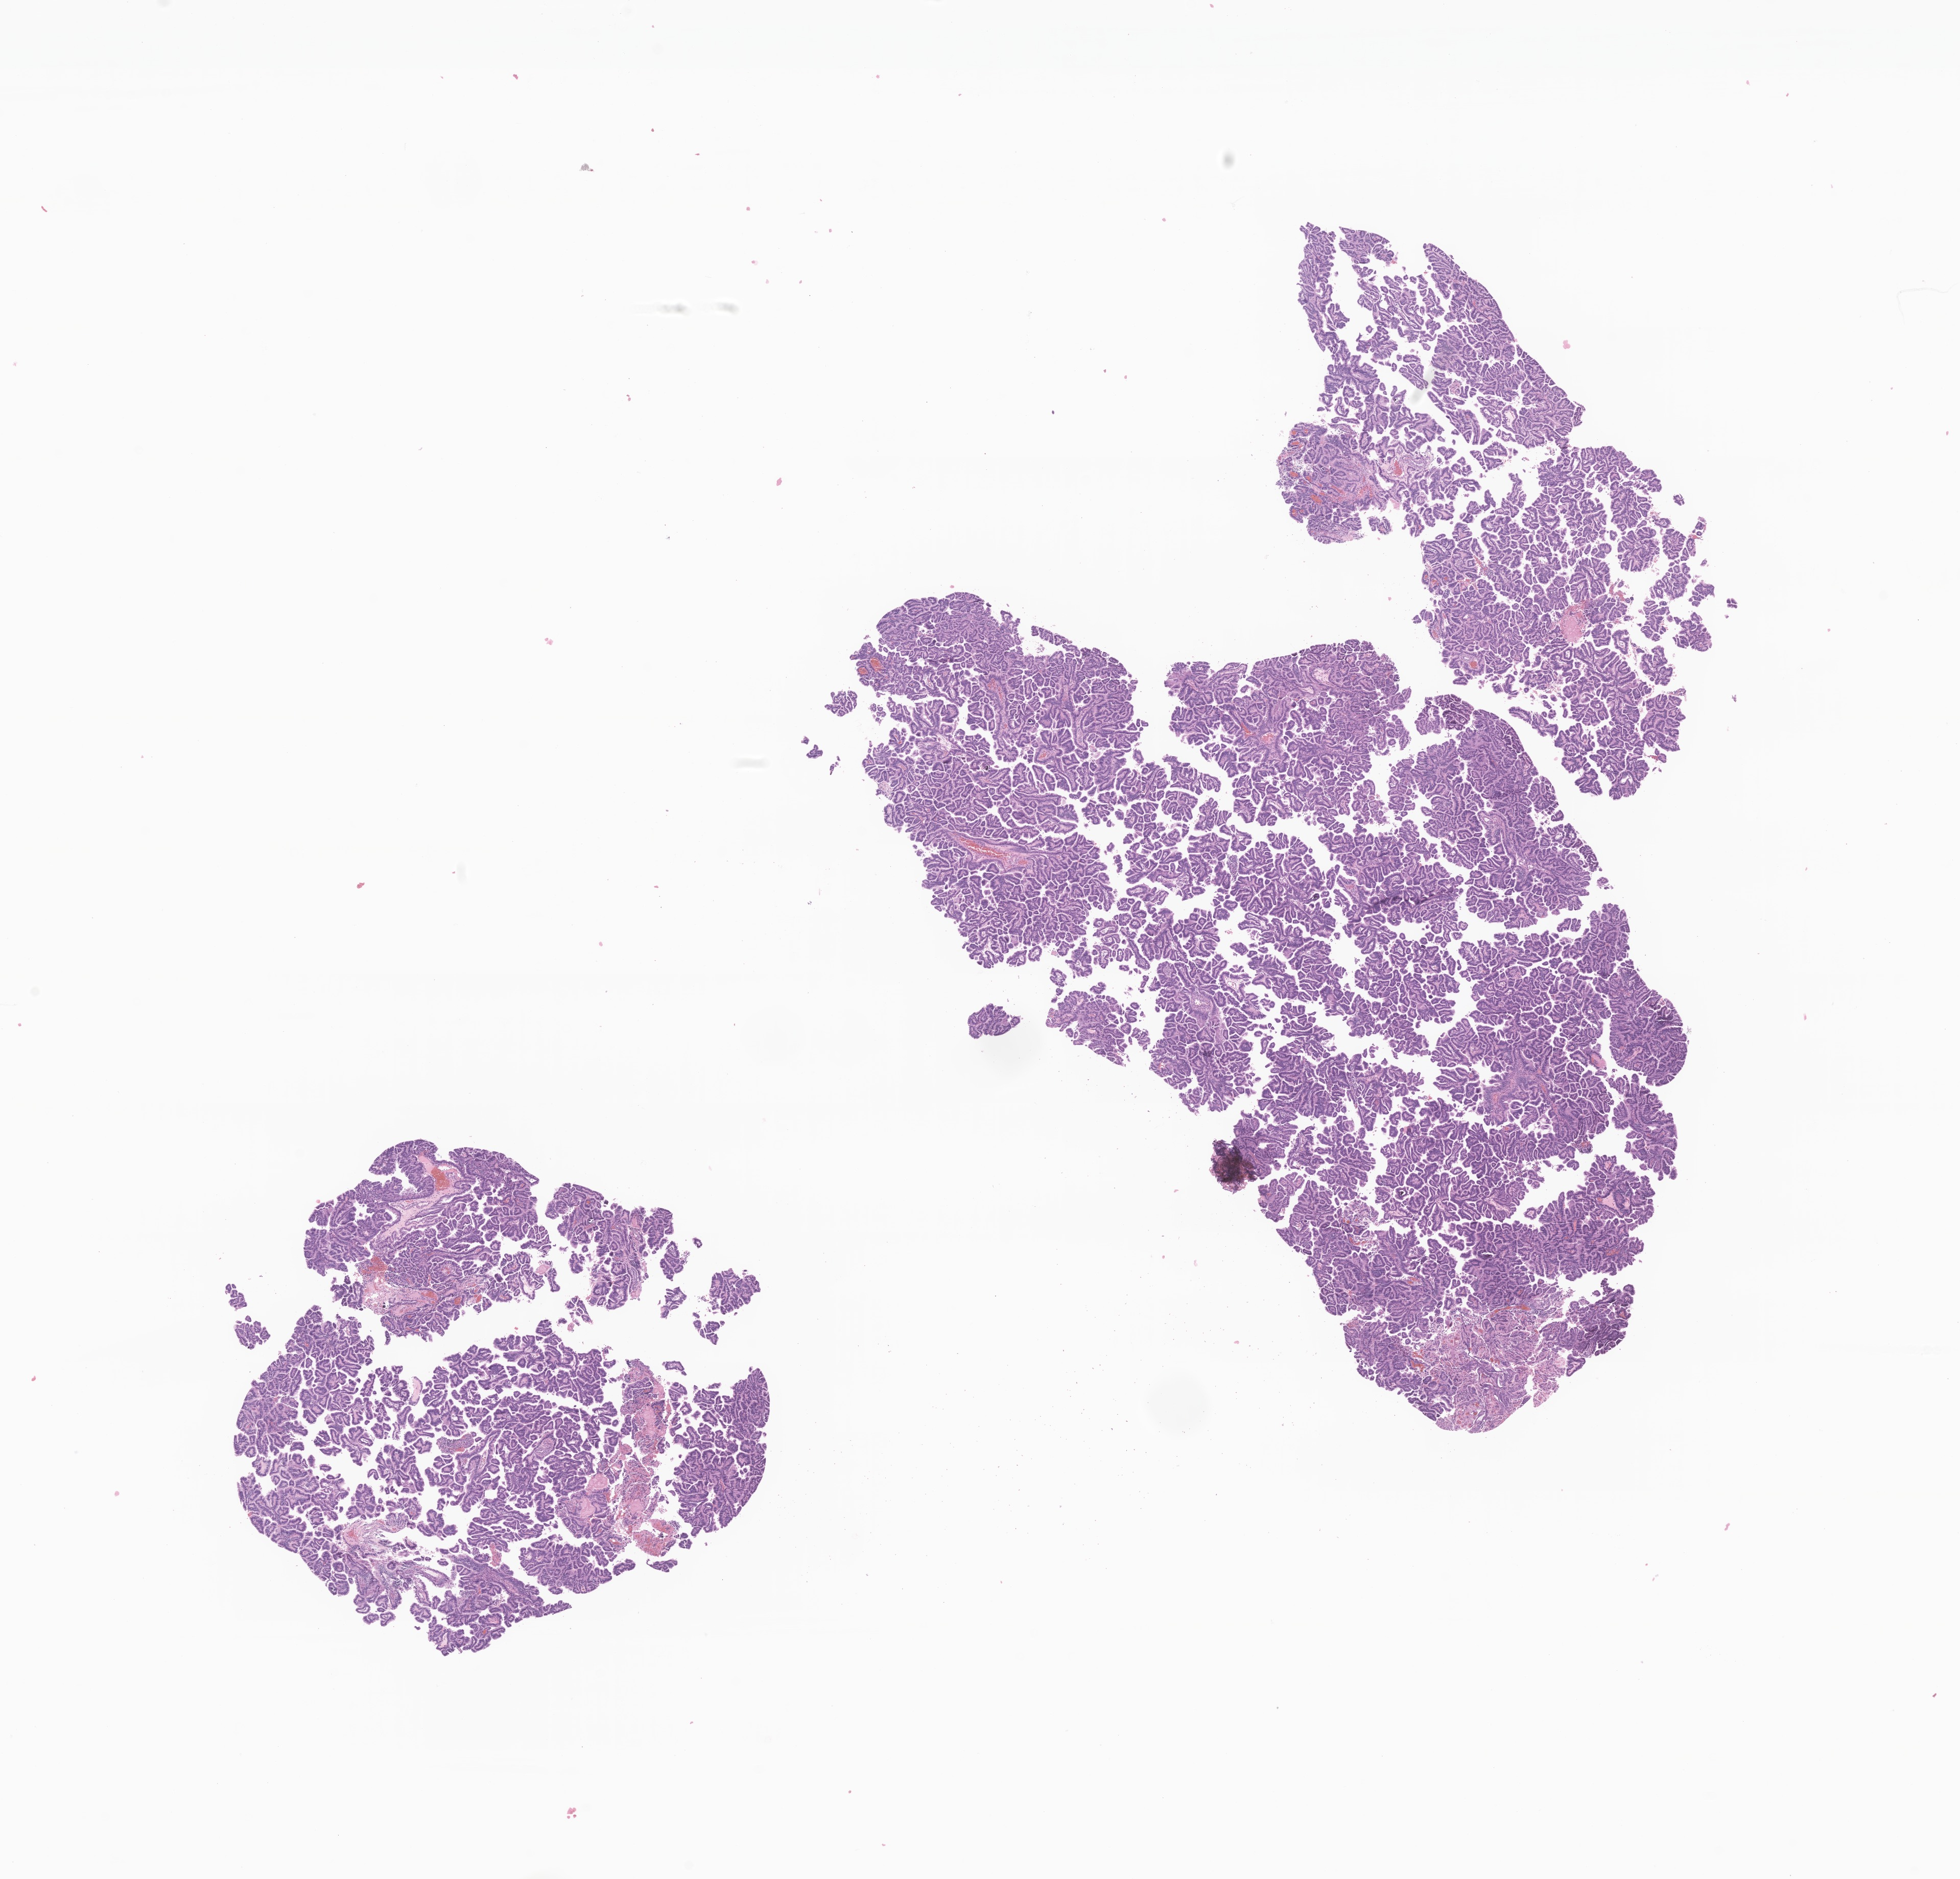
Whole-slide image, hematoxylin and eosin (H&E) stain of tumor tissue from the brain, a low-resolution overview of the entire scanned area, about 16.2 x 15.5 mm. Formalin-fixed paraffin-embedded section. Patient: male, age 179 months (14 years 11 months).
• diagnosis (ICD-O-3 morphology term): Choroid plexus papilloma, NOS